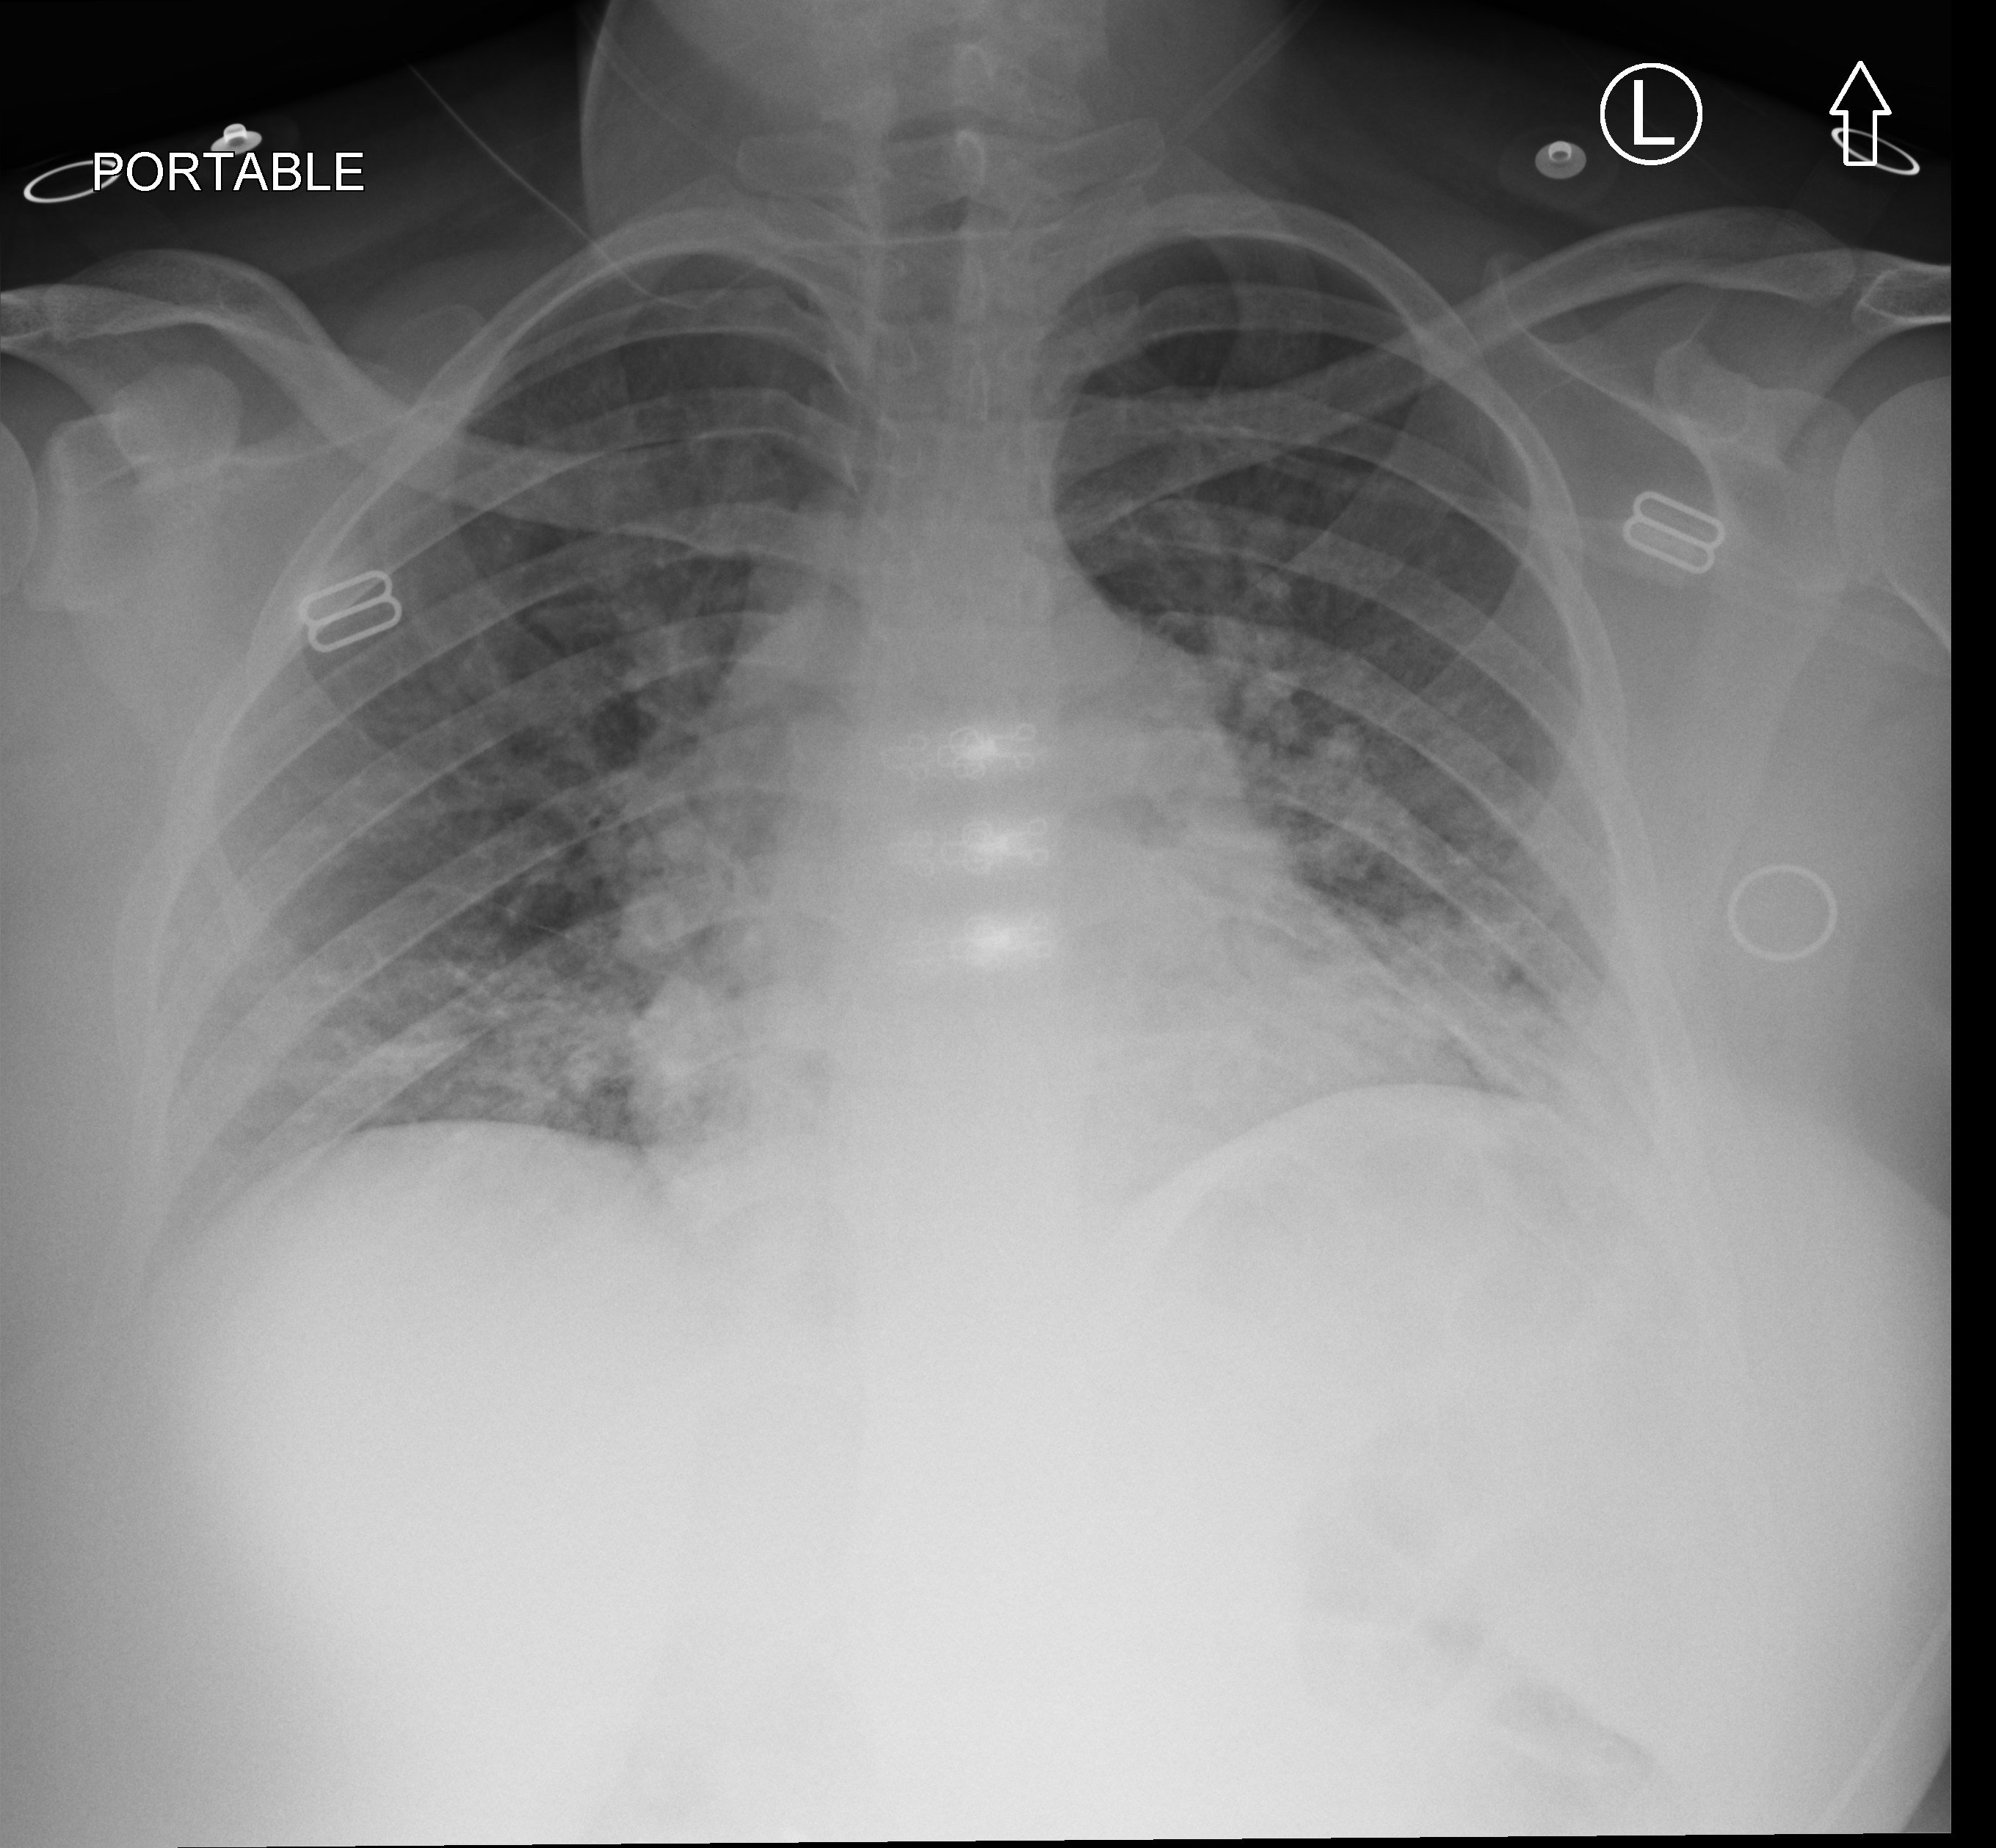
Chest X-ray (portable). Female patient hospitalised with COVID-19, age 18–59 years.
From the hospital-stay record, not from the radiograph (when in the stay this image was taken is not recorded): mechanically ventilated during this hospital stay: no; admitted to intensive care during this hospital stay: no; hypertension (admission record): no.